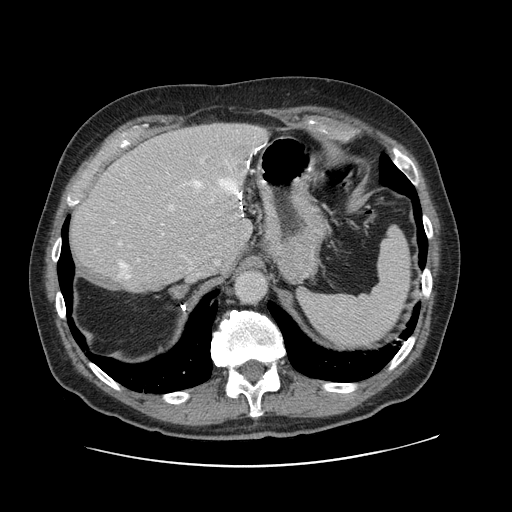
Contrast-enhanced abdominal CT, one axial slice. Position 86 of 138 along the scan axis. 120 kVp. Intravenous contrast given. Soft-tissue window (W 400 / L 40 HU). 2.5 mm slice thickness. 512 × 512 image matrix, field of view 402 × 402 mm. Male patient, age 71 years. Case-level facts recorded for this patient, not image findings: diagnosis: colorectal cancer liver metastases, imaged before liver resection; multiple liver metastases: no; largest metastasis: 3.3 cm; disease in both lobes: no.
Outlined on this slice (outlined manually by an expert reader):
- hepatic veins: bounding box [x1, y1, x2, y2] px = [119, 148, 259, 279]
- liver: [69, 124, 267, 293]
- planned liver remnant (the part of the liver to remain after resection): [70, 152, 241, 293]
- portal vein (with intrahepatic branches): [118, 162, 204, 246]